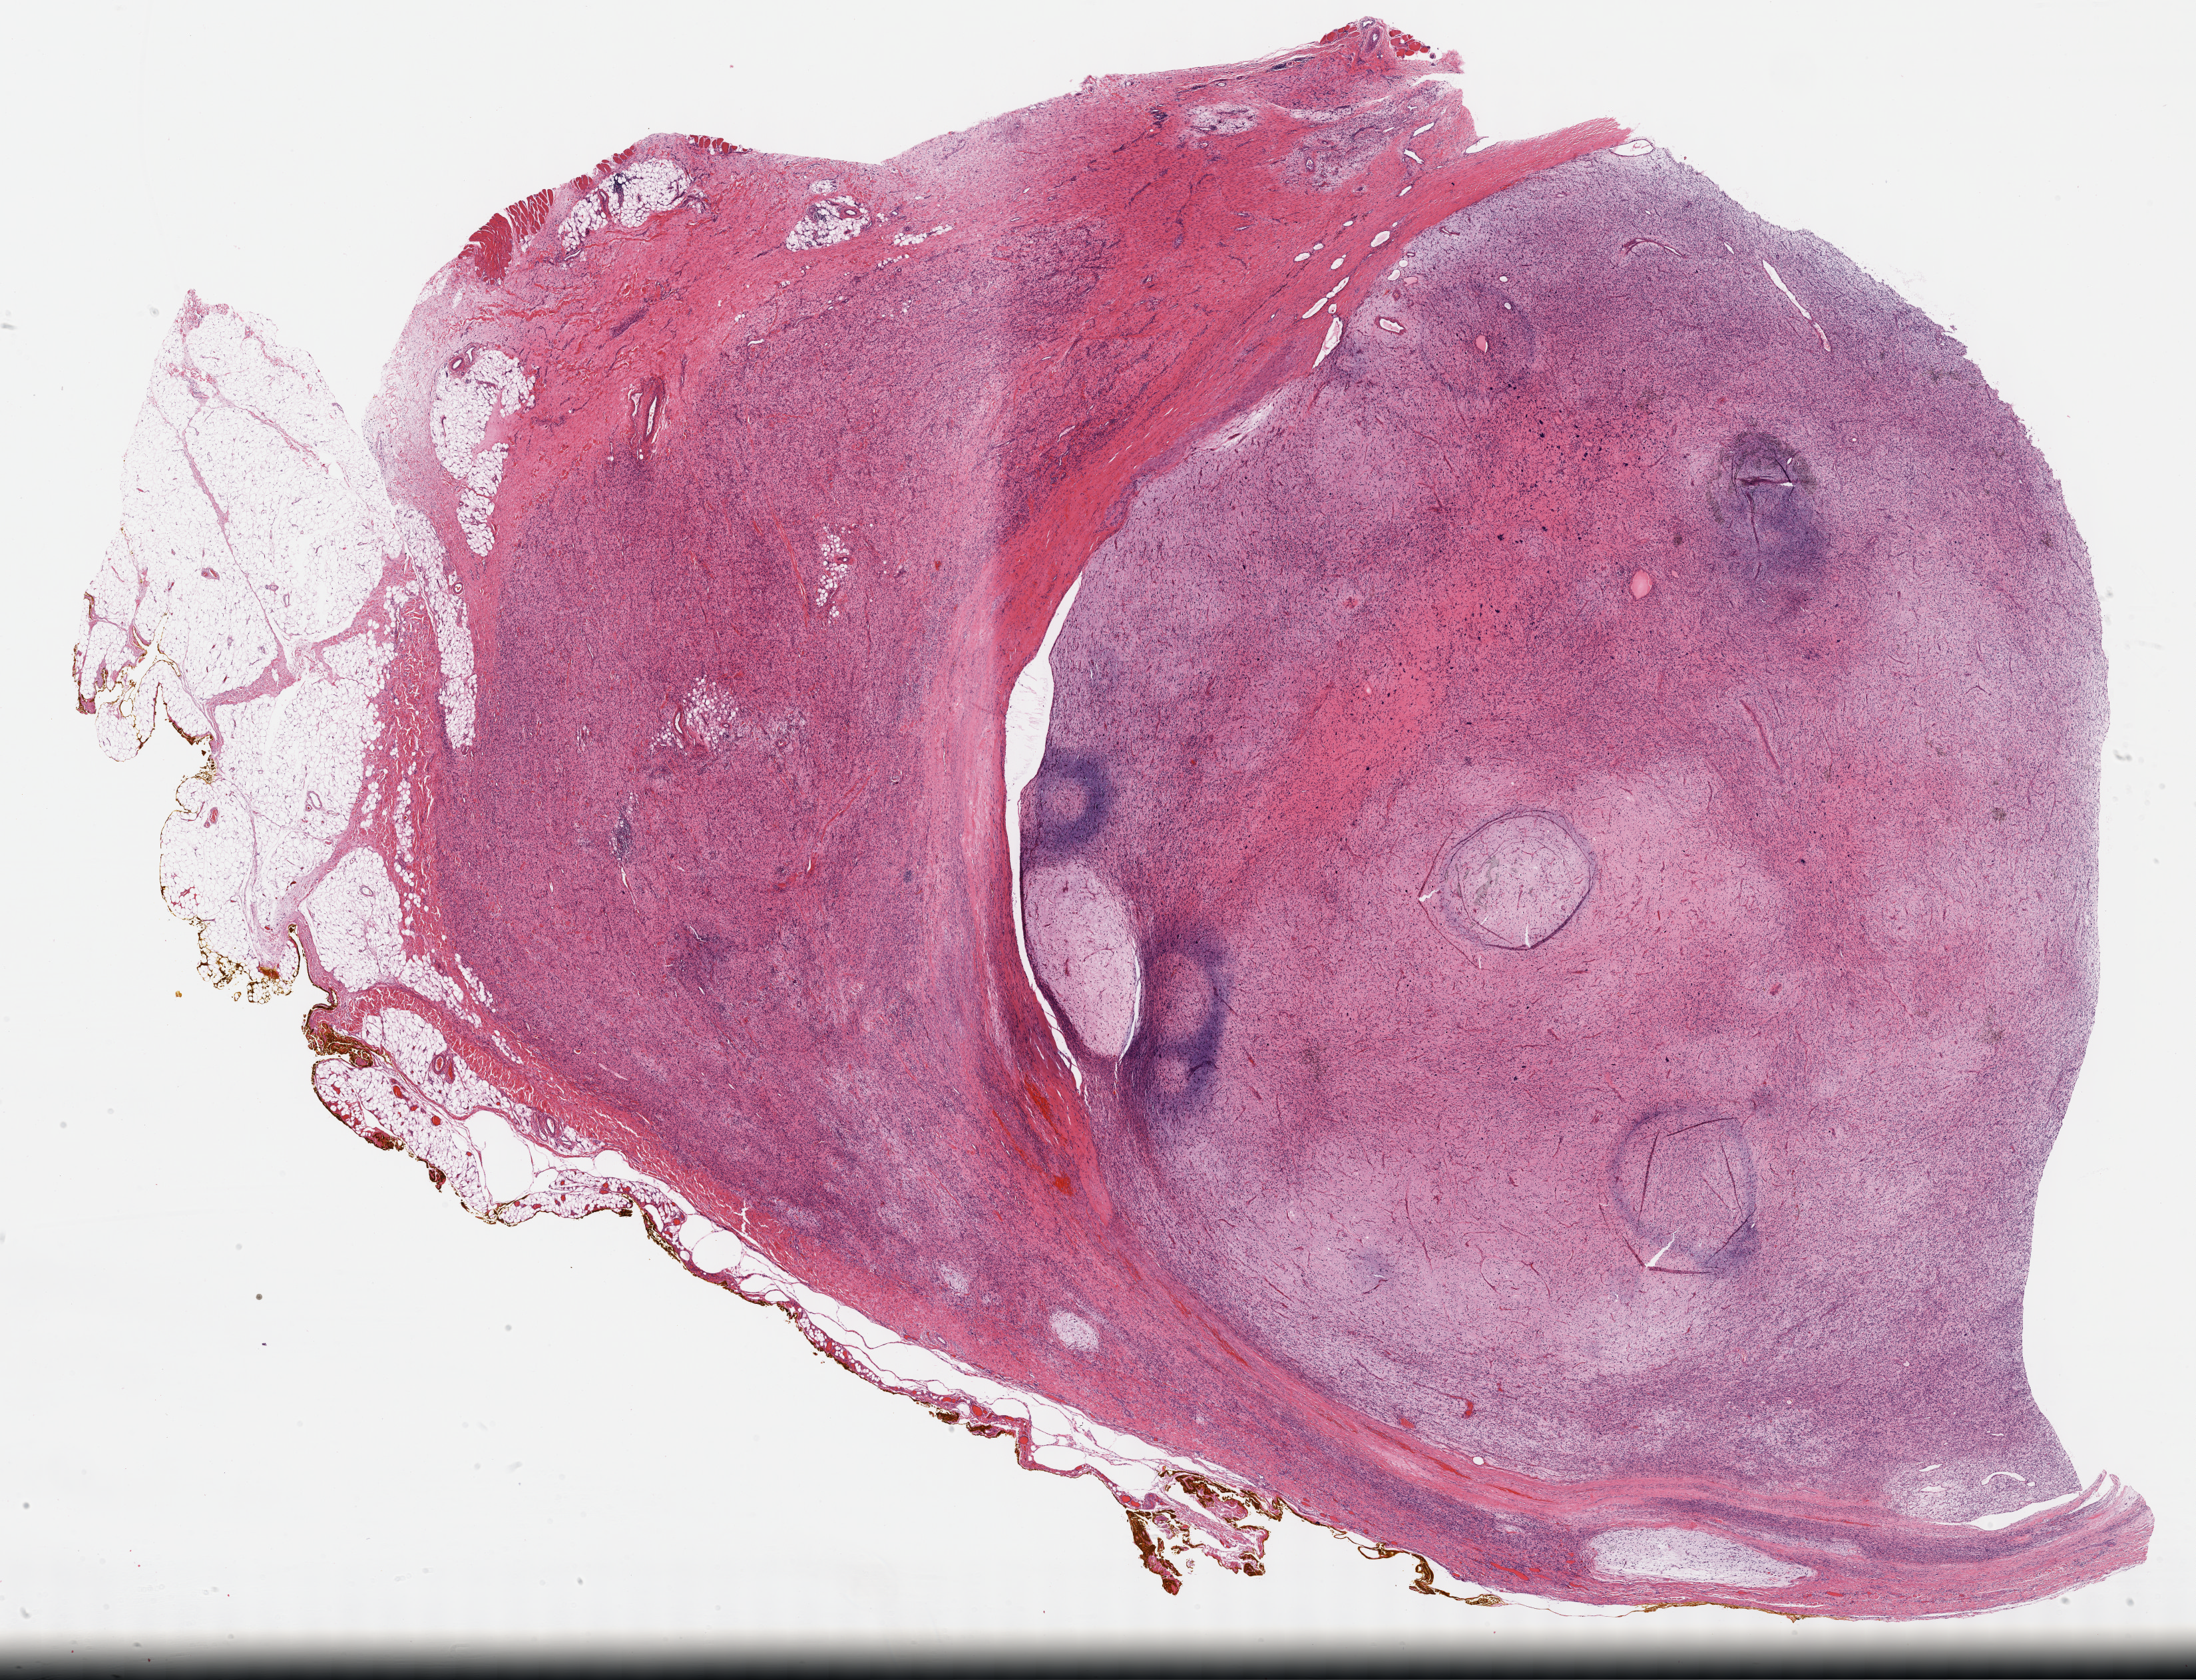
Digitized H&E tissue section (whole slide), a low-resolution overview of the entire scanned area, about 26.7 x 20.4 mm; formalin-fixed paraffin-embedded (FFPE) diagnostic section; connective, subcutaneous and other soft tissues, primary tumour sample. Patient: male, age at initial diagnosis 35 years.
Pathologic diagnosis: Fibromyxosarcoma (connective, subcutaneous and other soft tissues of lower limb and hip).